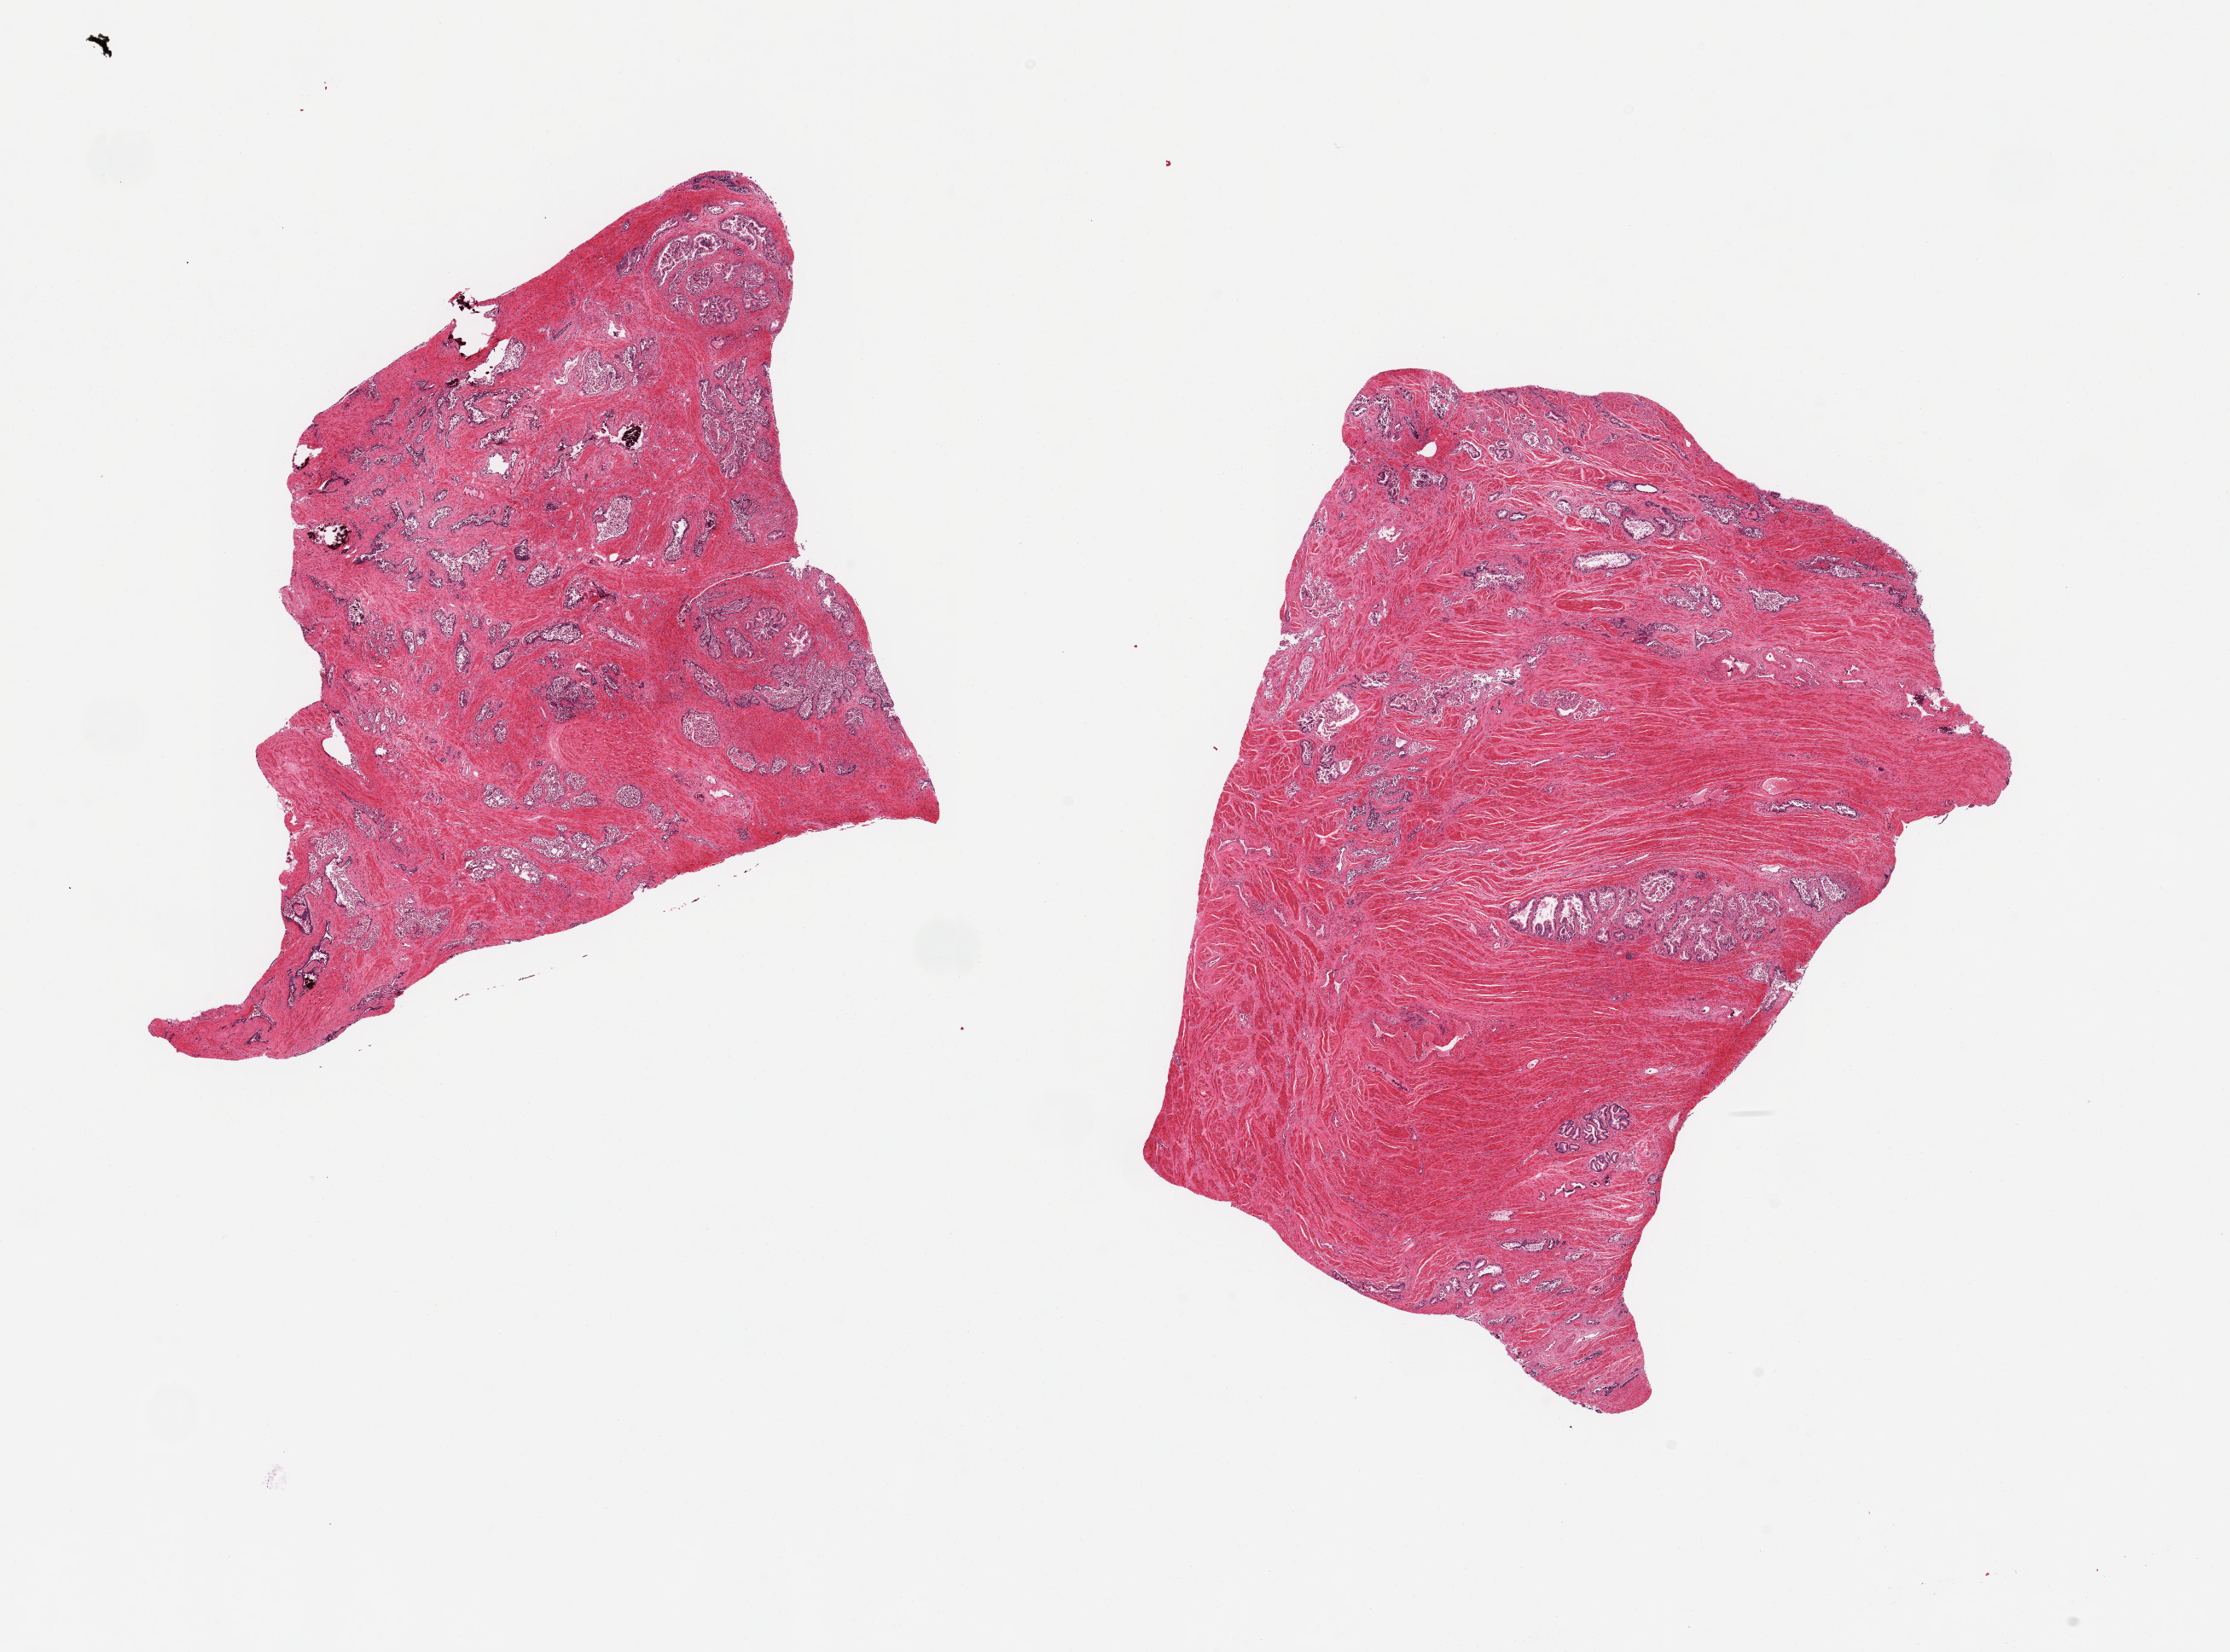
Whole-slide image, H&E stain, shown as a low-resolution overview of the whole scanned area (about 20.7 x 15.3 mm). PAXgene-fixed, paraffin-embedded tissue. Sampled site (target tissue): prostate. Donor tissue sample. Donor sex: male.
Pathologist's review note for this sample: 2 pieces, glands with moderately advanced autolysis.